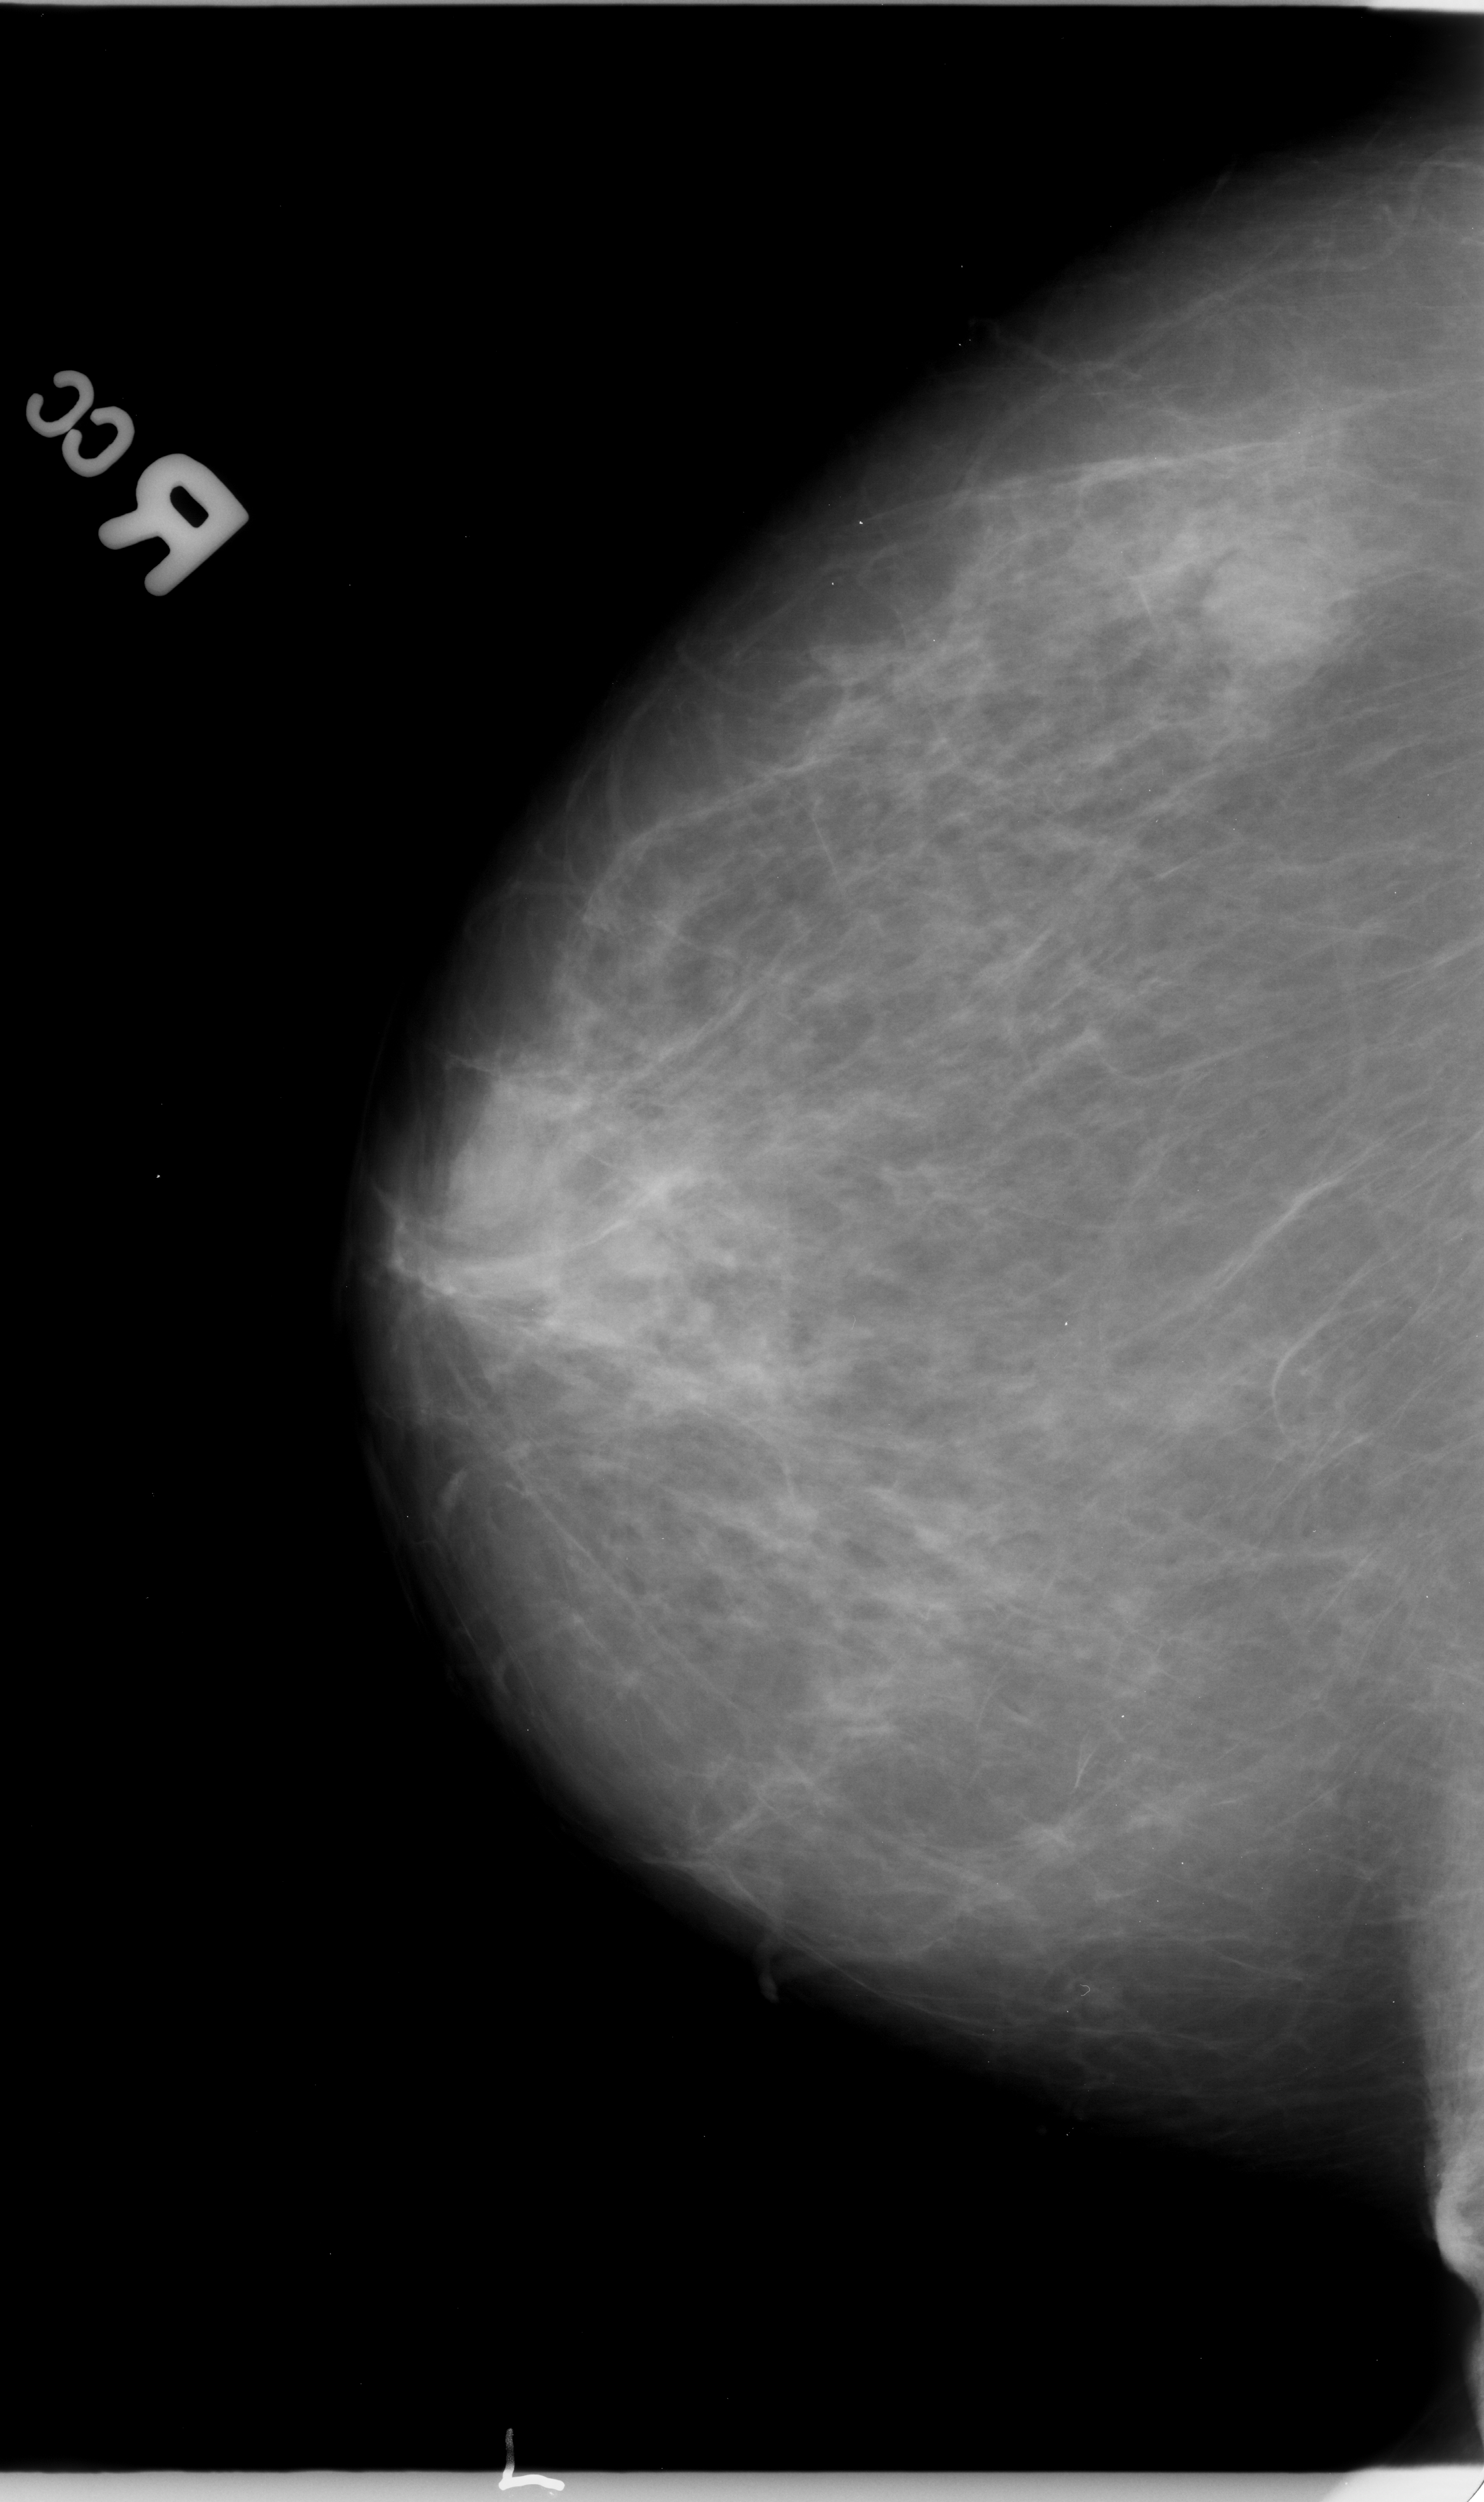
Mammogram (digitized film), right breast, CC view, BI-RADS breast density category 3 (scale 1–4).
Radiologist-marked abnormalities on this image: mass, shape round, margins circumscribed; BI-RADS assessment category 3; subtlety rating 4 on a 1 (subtle) to 5 (obvious) scale; pathology (as recorded): benign.